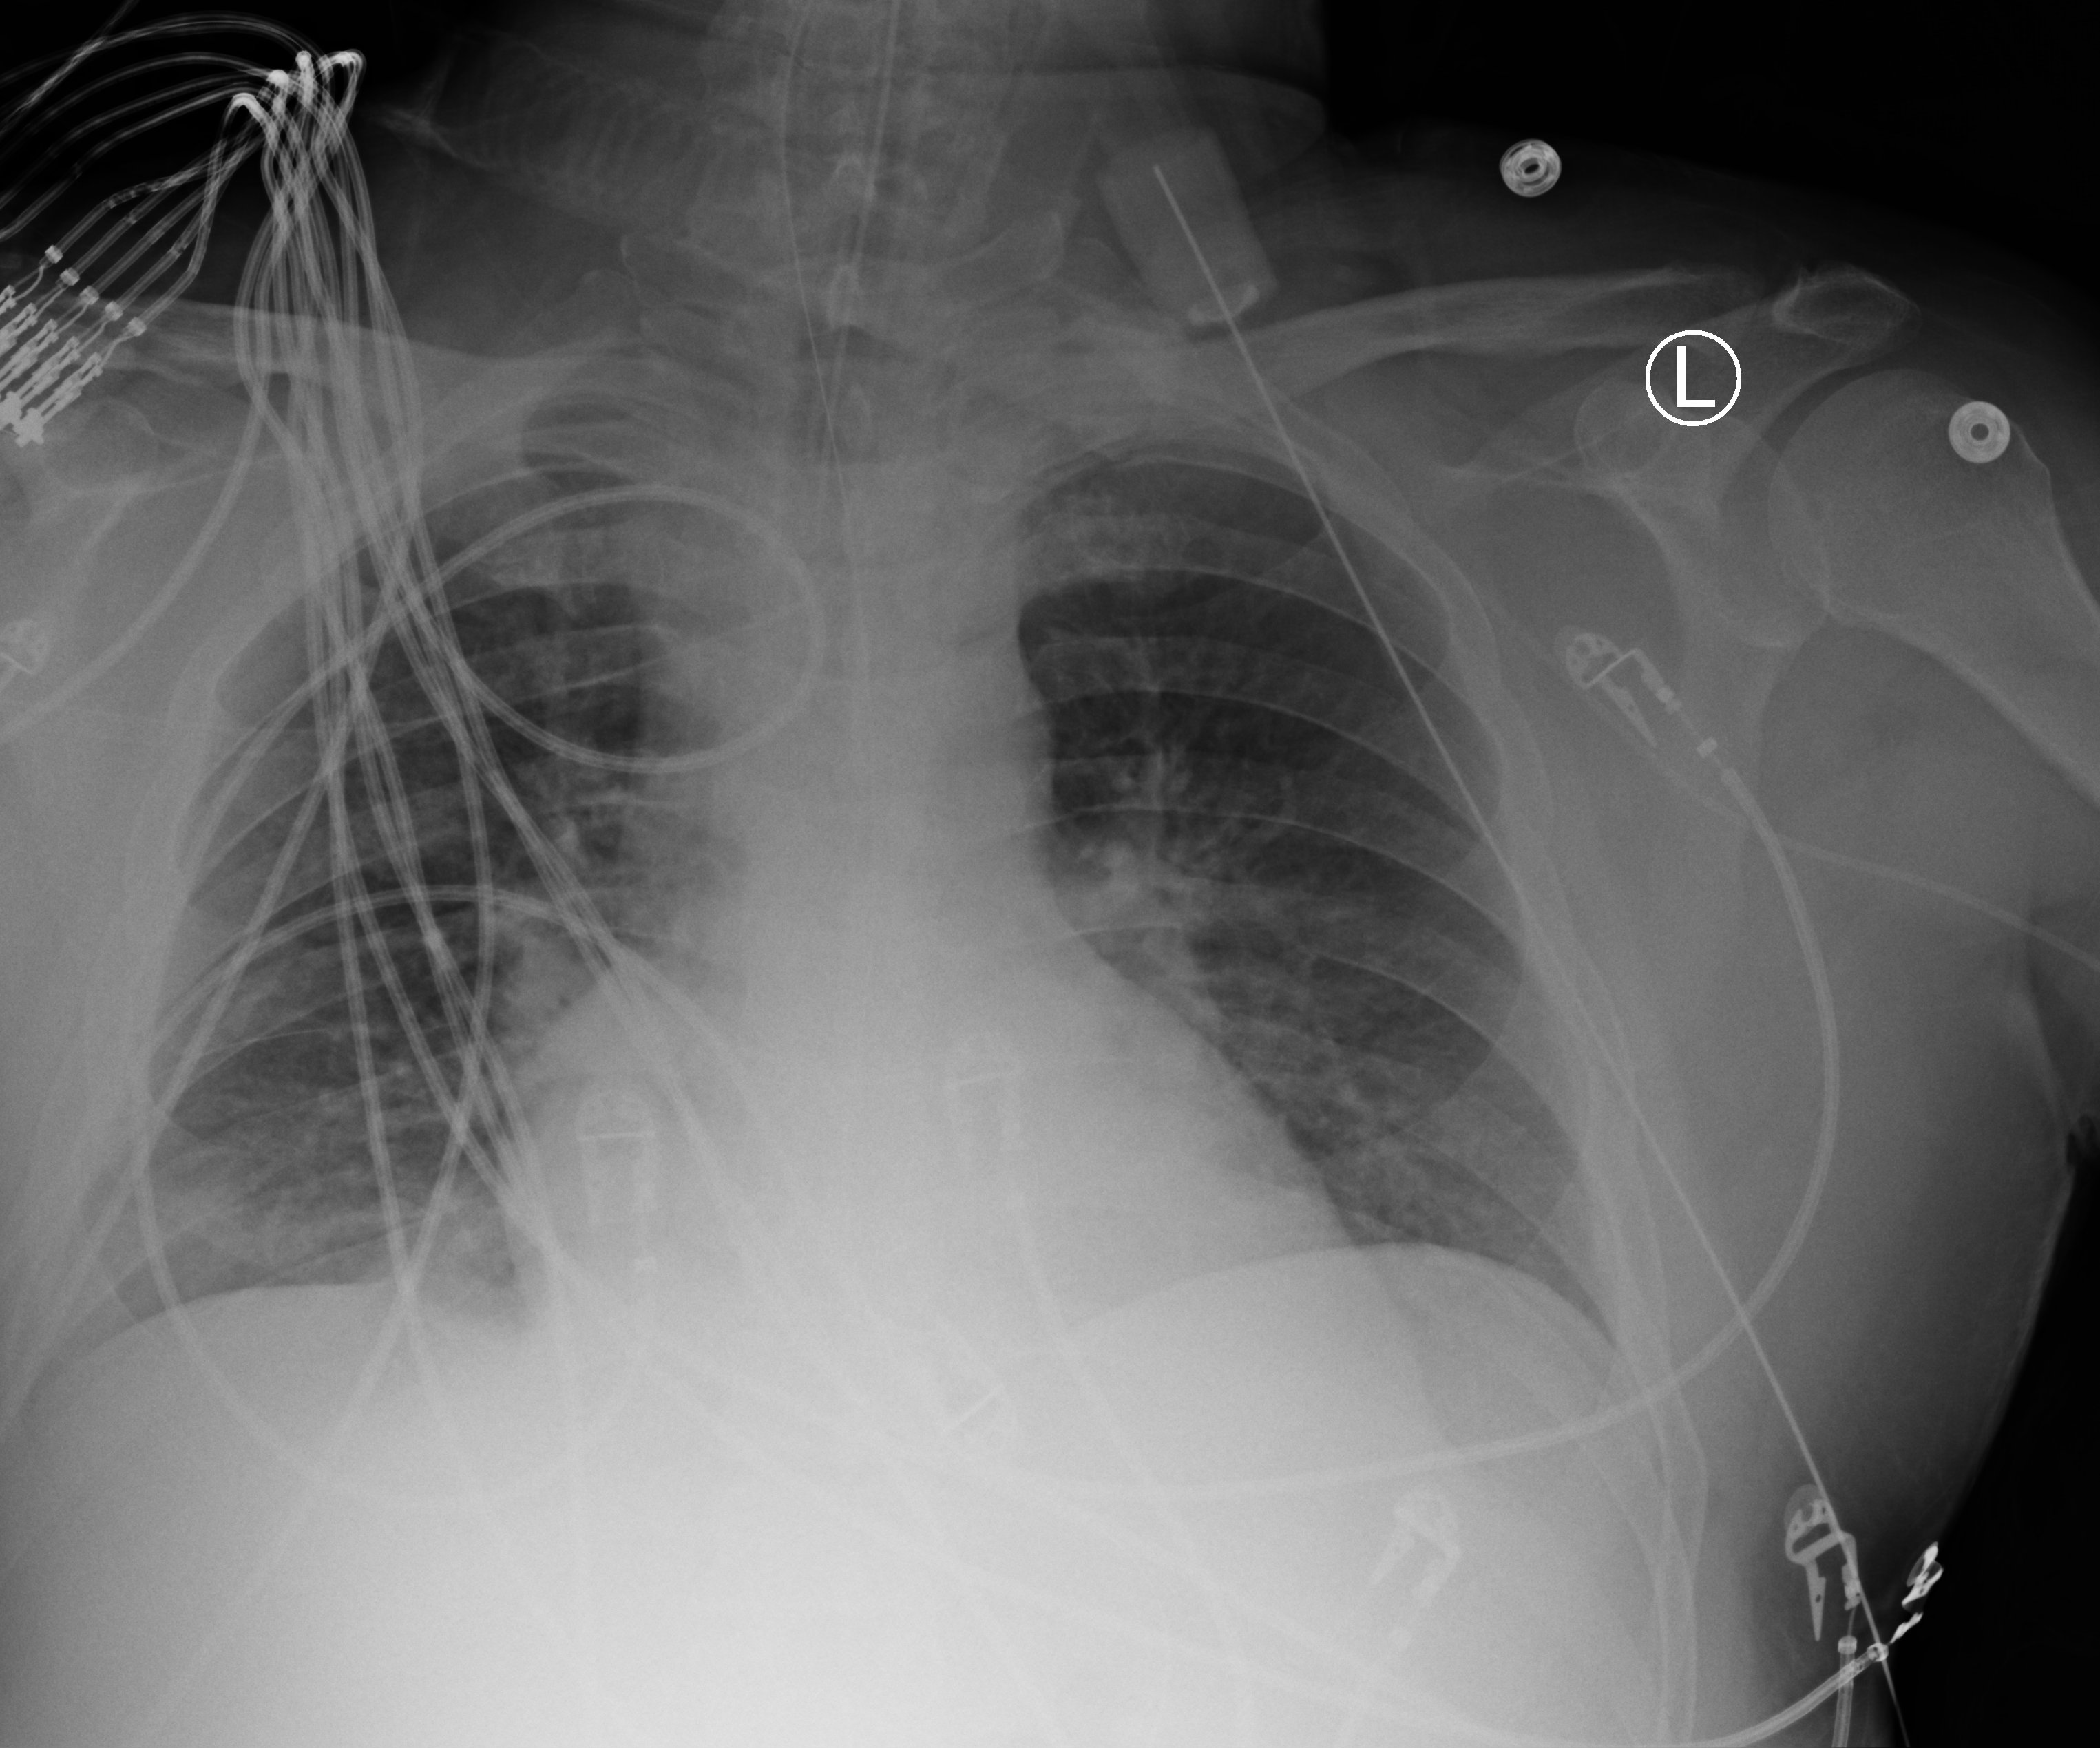
Bedside chest radiograph (computed radiography). Male patient hospitalised with COVID-19, age 18–59 years.
Hospital-stay facts (about this admission, not read from this image; timing relative to this image not recorded): length of hospital stay: 65 days; mechanically ventilated during this hospital stay: yes.